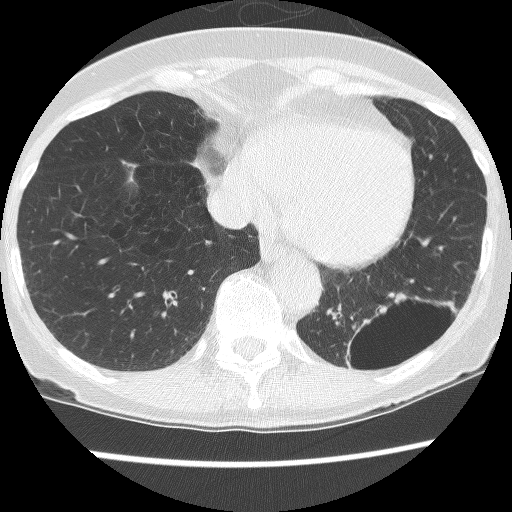
Low-dose screening chest CT, axial slice, third screening round (two years after baseline), lung window (W 1500 / L -600 HU), 2.5 mm slice thickness, lung (sharp) reconstruction kernel (BONE), slice 94 of 130 in the series. Female, age 61 years at enrolment. Current smoker at enrolment.
Lesion marked by an expert reader, bounding box (x1, y1, x2, y2) in pixels: (333, 293, 444, 388). The screening reader recorded 2 non-calcified nodules or masses ≥4 mm on this exam (left lower lobe, left lower lobe); which of them this box marks is not recorded. Official screen result: positive, no significant change: stable abnormalities potentially related to lung cancer, unchanged since the prior screening exam.